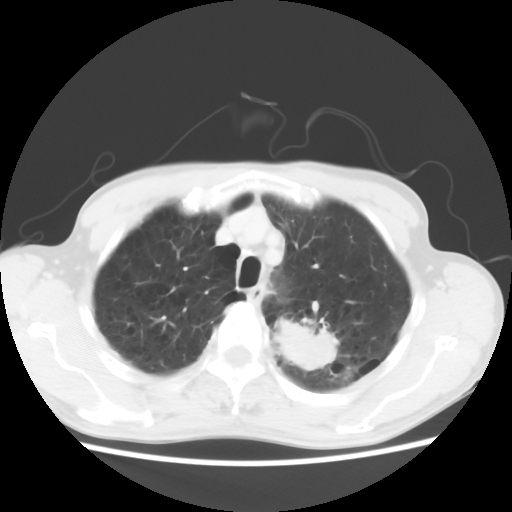
Chest CT, one axial slice. Position 51 of 64 along the scan axis. Reconstruction kernel STANDARD. 120 kVp. Lung window (W 1500 / L -600 HU). 5 mm slice thickness. 512 × 512 image matrix, field of view 346 × 346 mm. Male patient, age 63 years. Case-level facts recorded for this patient, not image findings: clinical TNM (as recorded): T2 N0 M0.
Outlined on this slice (rectangle marked by the reading radiologist):
- lung tumour (recorded histology: adenocarcinoma): bounding box <272,311,343,384> (left, top, right, bottom; pixels)